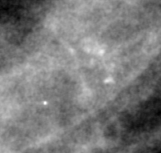
Cropped region of a digitized screen-film mammogram centred on a radiologist-marked abnormality; left breast; CC view.
Calcifications, morphology pleomorphic, distribution clustered; BI-RADS assessment category 4; pathology result (as recorded, not read from the image): benign.